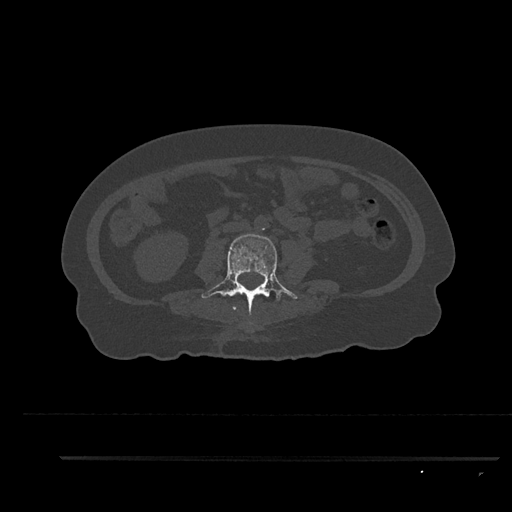
CT including the spine, one axial slice. Reconstruction kernel Br40s/3. 120 kVp. Bone window (W 1800 / L 400 HU). 0.5 mm slice thickness. 512 × 512 image matrix, field of view 408 × 408 mm. Female patient, age 44 years. Case-level facts recorded for this patient, not image findings: primary cancer: renal; vertebrae with lytic lesions (as recorded): L1.
Structures marked on this image (semi-automatic segmentation, software-assisted and operator-edited):
- L2 vertebra: bounding box (x1, y1, x2, y2) in pixels: (233, 307, 236, 310)
- L3 vertebra: (202, 234, 298, 315)